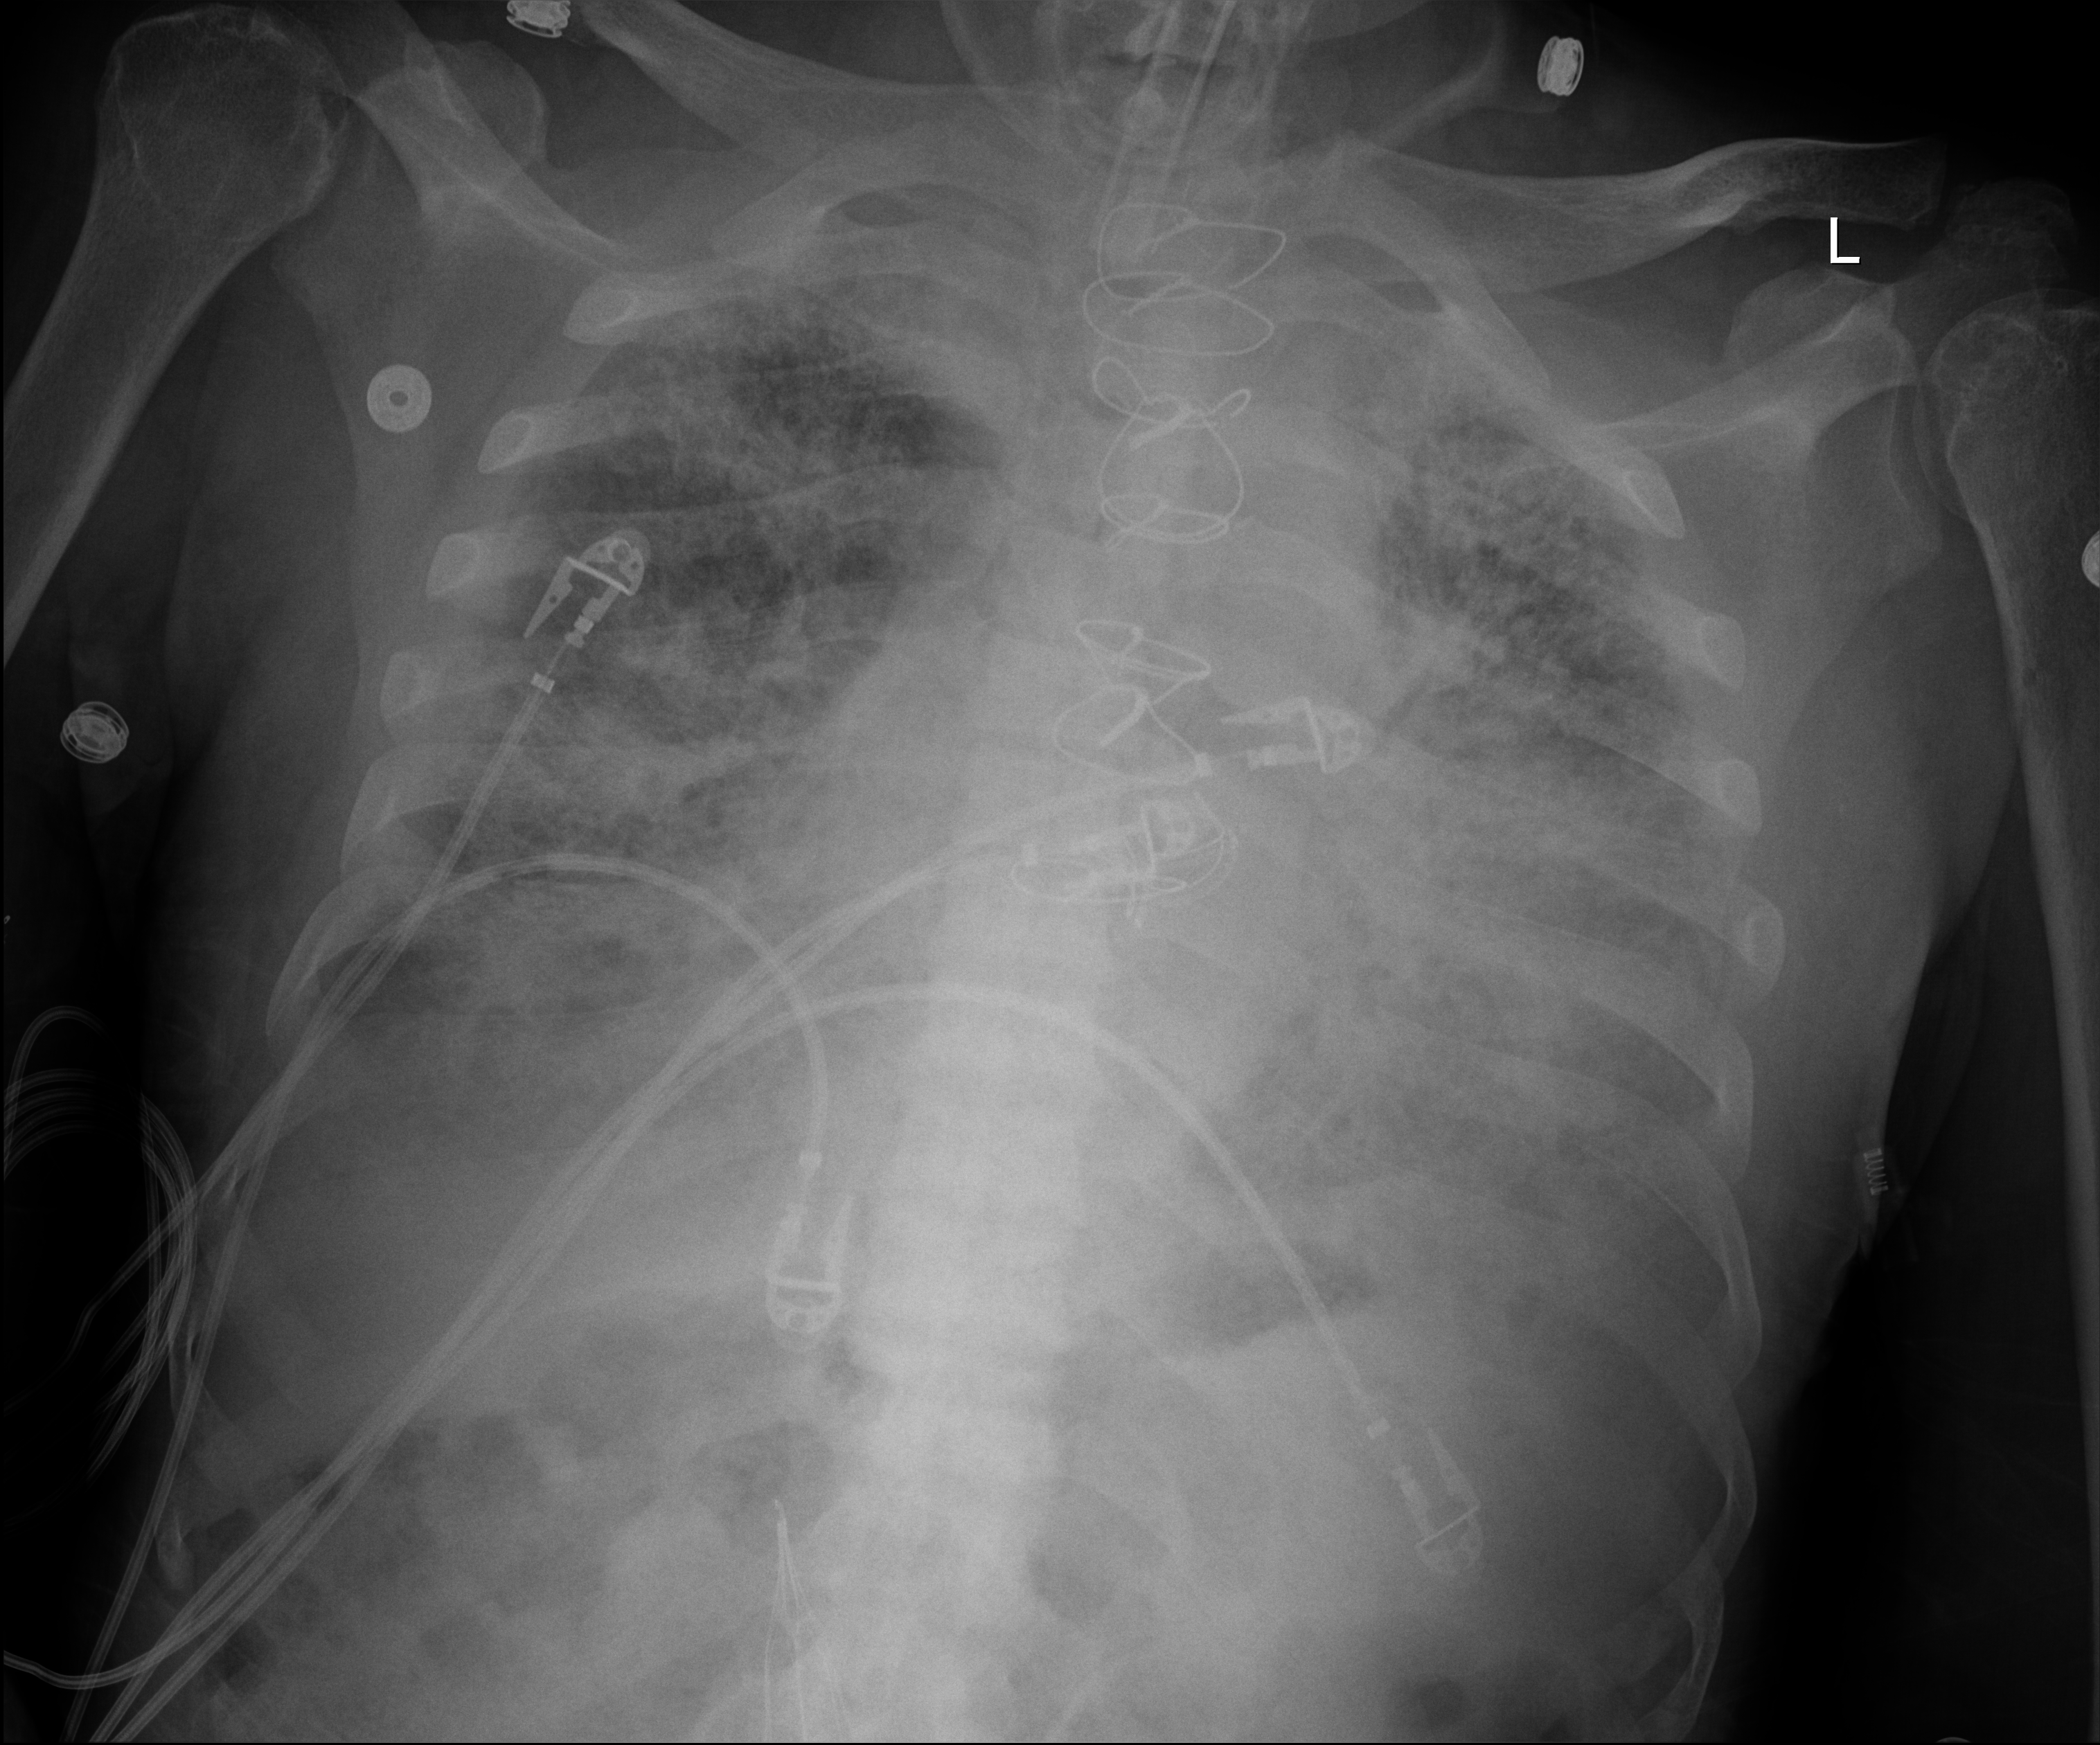
Bedside chest radiograph (digital radiography); anteroposterior (AP) projection. Male patient hospitalised with COVID-19, age 60–74 years.
Hospital-stay facts (about this admission, not read from this image; timing relative to this image not recorded):
- length of hospital stay: 50 days
- admitted to intensive care during this hospital stay: yes